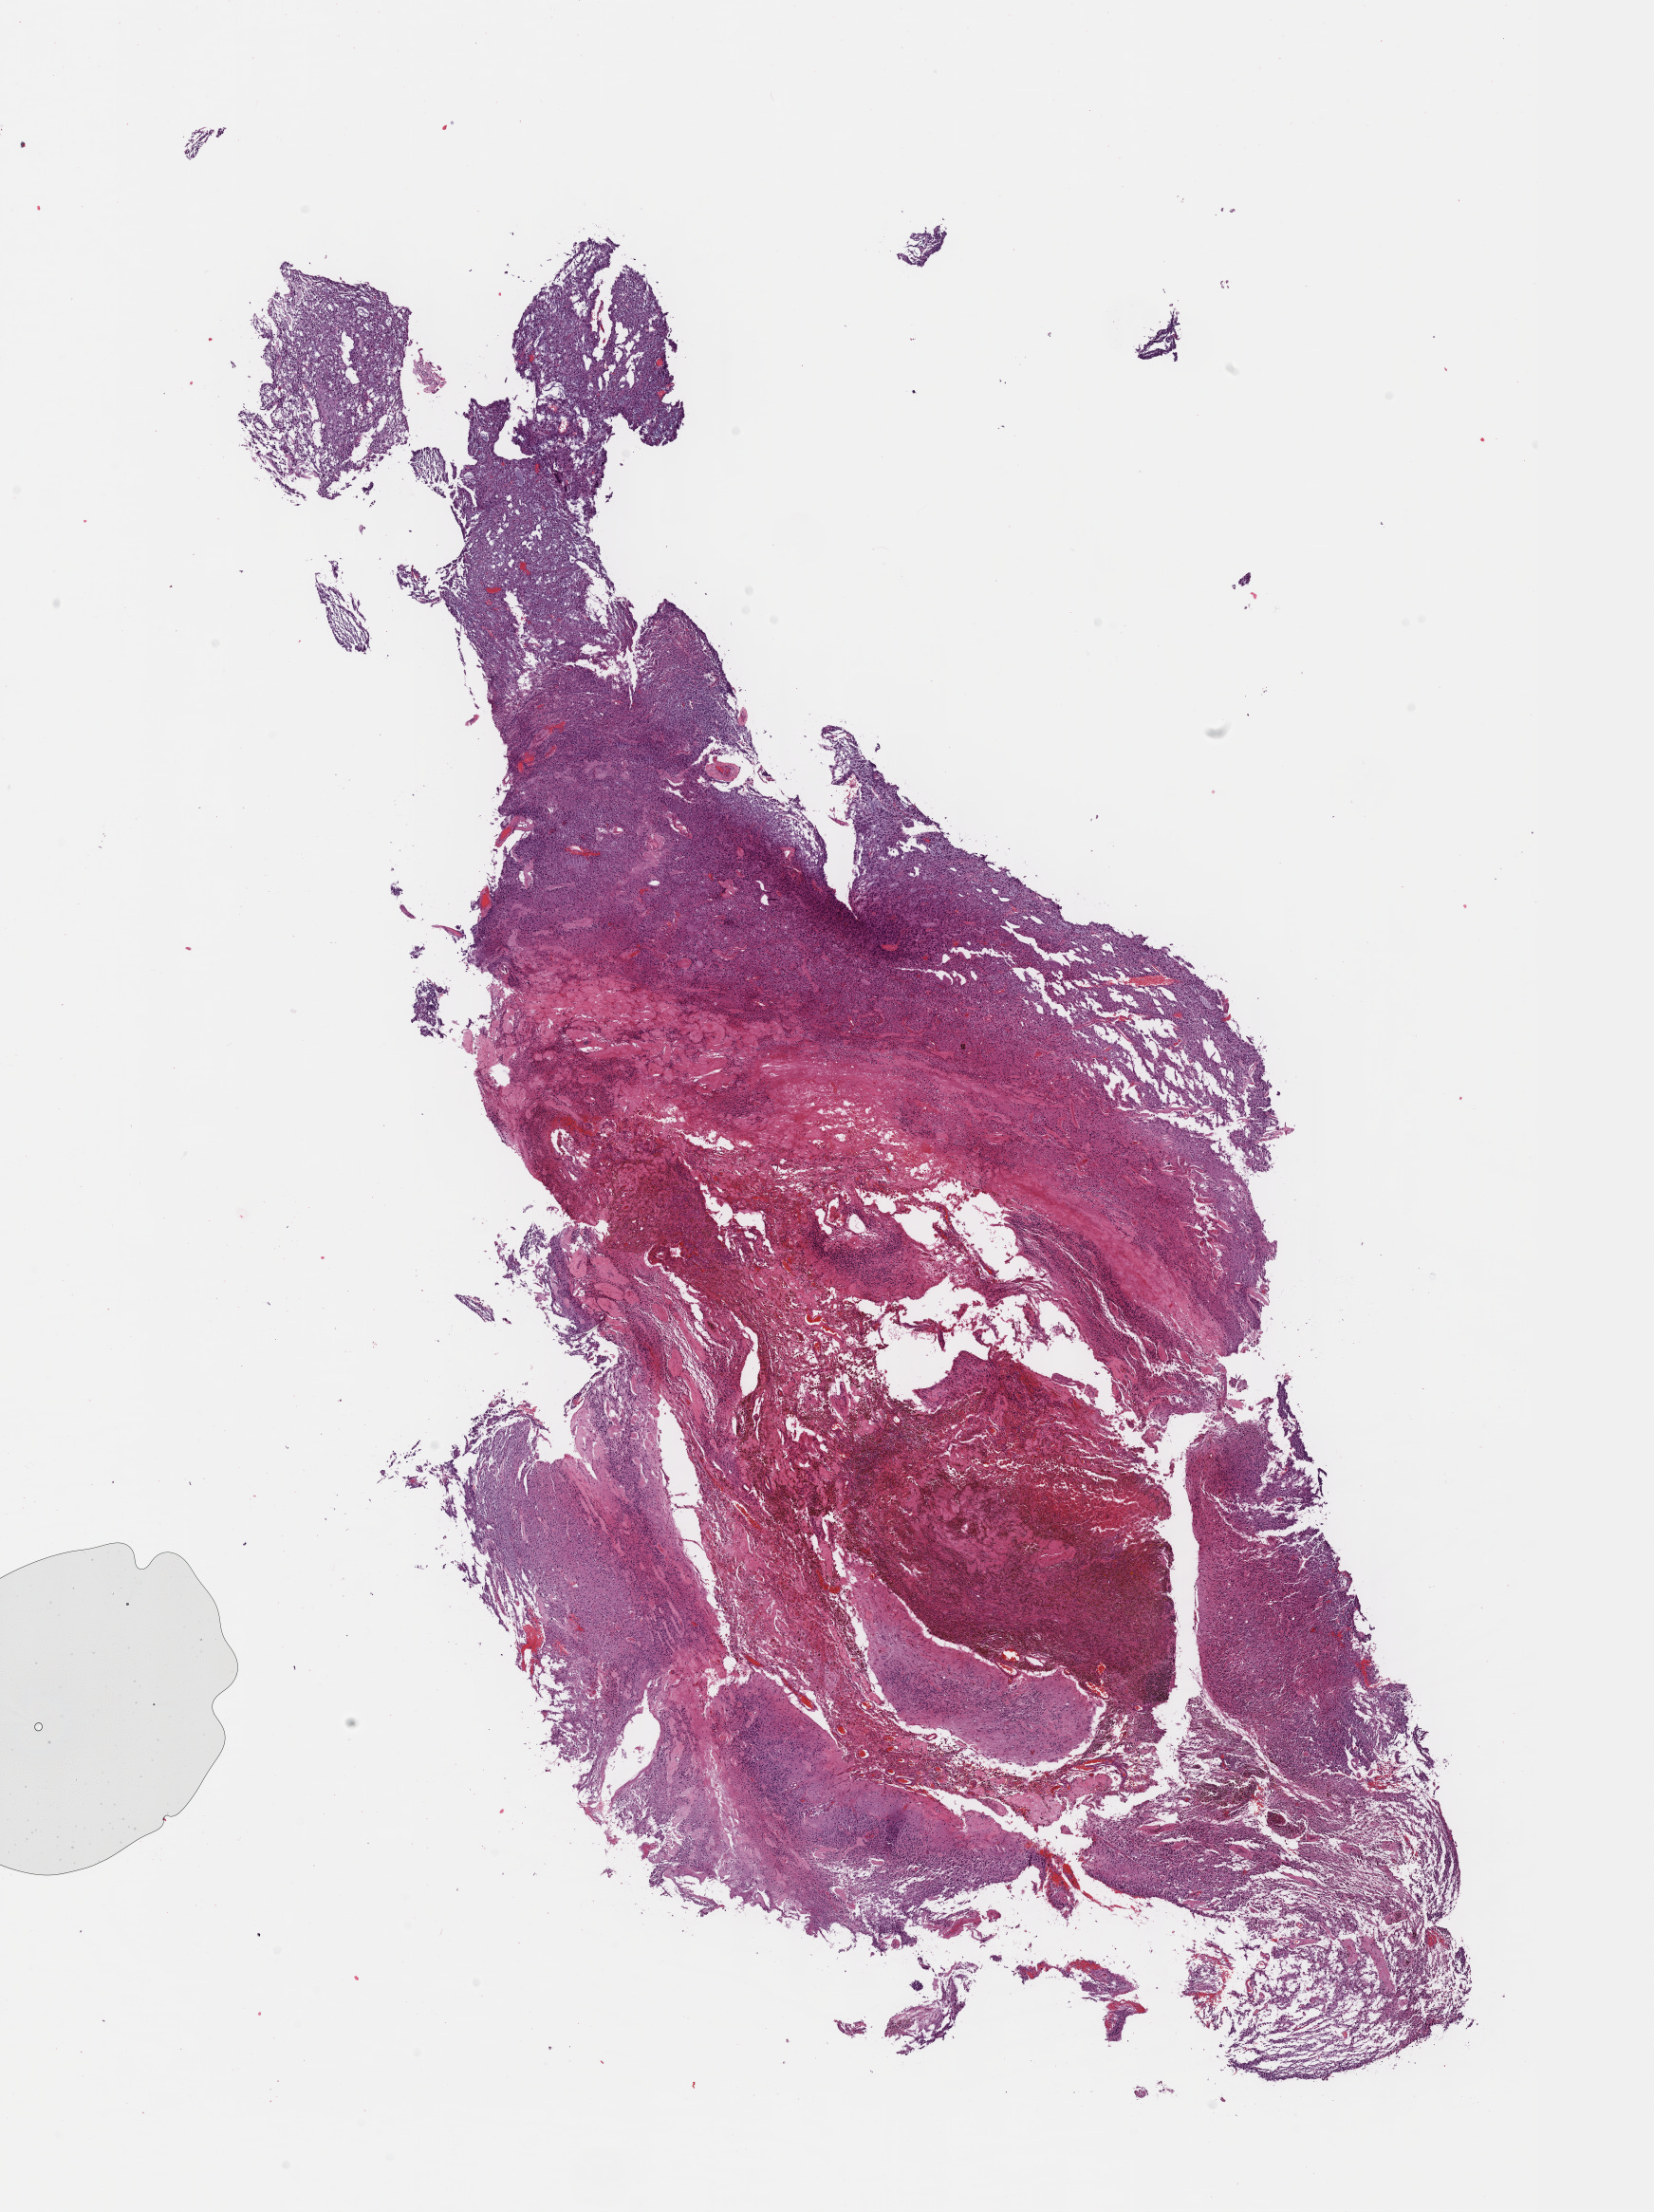
Hematoxylin and eosin (H&E) stained whole-slide image, shown as a low-resolution overview of the whole scanned area (about 14.1 x 18.8 mm). Formalin-fixed paraffin-embedded (FFPE) diagnostic section. Brain, primary tumour sample. Female, age 51 years at initial diagnosis. Histologic grade: G2 (moderately differentiated).
- pathologic diagnosis: Oligodendroglioma, NOS (cerebrum)